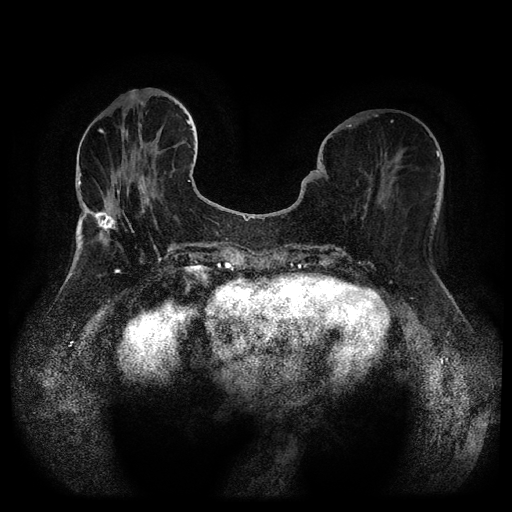
Breast MRI (dynamic contrast-enhanced, multi-phase), one axial slice; position 36 of 116 along the scan axis; dynamic contrast-enhanced series, time point 2 of 5 at this slice position (early post-contrast); 1.5 T; TE 2.6 ms, TR 5.3 ms; 2 mm slice thickness; 512 × 512 image matrix. Patient: female, 75 years.
Annotated regions visible in this slice (semi-automatic segmentation, software-assisted and operator-edited):
- breast lesion (labelled benign in the annotation): bounding box [x1, y1, x2, y2] px = [136, 175, 147, 200]
- breast lesion (labelled benign in the annotation): [85, 208, 119, 234]